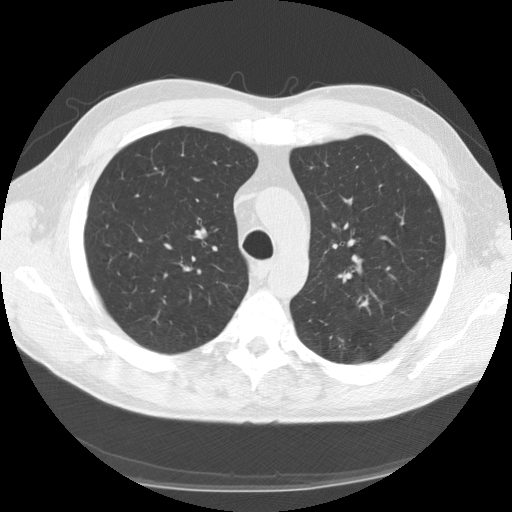
Low-dose screening chest CT, axial slice. Second annual screen. Lung window (W 1500 / L -600 HU). 120 kVp. Slice 39 of 152 in the series. 512 × 512 image matrix, field of view 370 × 370 mm. Male, age 57 years at enrolment. Current smoker at enrolment.
Expert reader's lesion annotation, bounding box <341,285,381,324> (left, top, right, bottom; pixels). The exam's reader record, not a measurement of the box and not confirmed to be the same lesion: non-calcified nodule or mass ≥4 mm, left upper lobe, 12 × 7 mm, spiculated (stellate) margins, mixed attenuation, pre-existing on the prior screen: no. Lung cancer was diagnosed 419 days after this screen (after the third annual screen): adenosquamous carcinoma, left upper lobe, poorly differentiated (G3), stage IA (AJCC 6th edition), 15 mm at pathology.